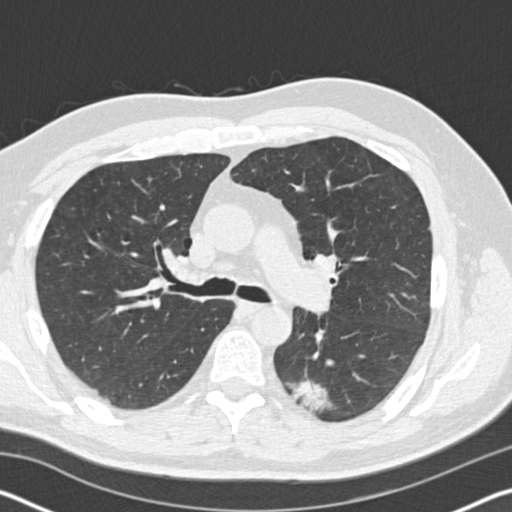
Chest CT (low-dose screening protocol), one axial image. Baseline annual screen. Lung window (W 1500 / L -600 HU). 2 mm slice thickness. Standard (soft-tissue) reconstruction kernel (B30f). 120 kVp. Slice 70 of 178 in the series. 512 × 512 image matrix. Male participant, aged 60 years at enrolment. Current smoker at enrolment.
Lesion marked by an expert reader, bounding box (x1, y1, x2, y2) in pixels: (276, 366, 357, 425). The screening reader recorded 3 non-calcified nodules or masses ≥4 mm on this exam (left lower lobe, right lower lobe, right lower lobe); which of them this box marks is not recorded. Participant outcome: lung cancer diagnosed 171 days after this screen — papillary adenocarcinoma, NOS, left lower lobe, moderately differentiated (G2), stage IB (AJCC 6th edition), 35 mm at pathology.